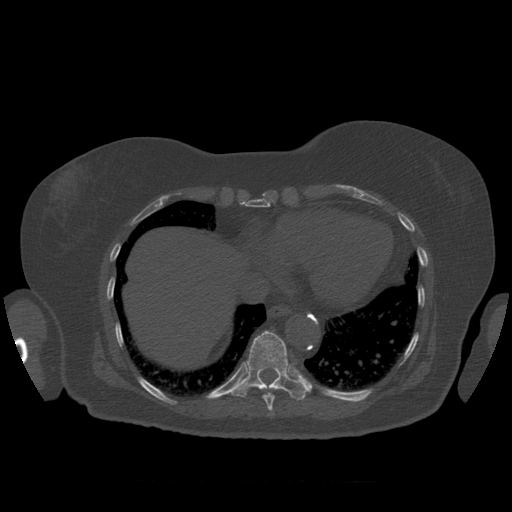
CT including the spine, one axial slice. Position 346 of 399 along the scan axis. 120 kVp. Bone window (W 1800 / L 400 HU). 512 × 512 image matrix, field of view 404 × 404 mm. Patient age 81 years. Case-level facts recorded for this patient, not image findings: primary cancer: renal; vertebrae with lytic lesions (as recorded): L1.
Structures marked on this image (semi-automatic segmentation, software-assisted and operator-edited):
- T10 vertebra: bounding box (x1, y1, x2, y2) in pixels: (232, 331, 311, 400)
- T9 vertebra: (263, 393, 275, 412)